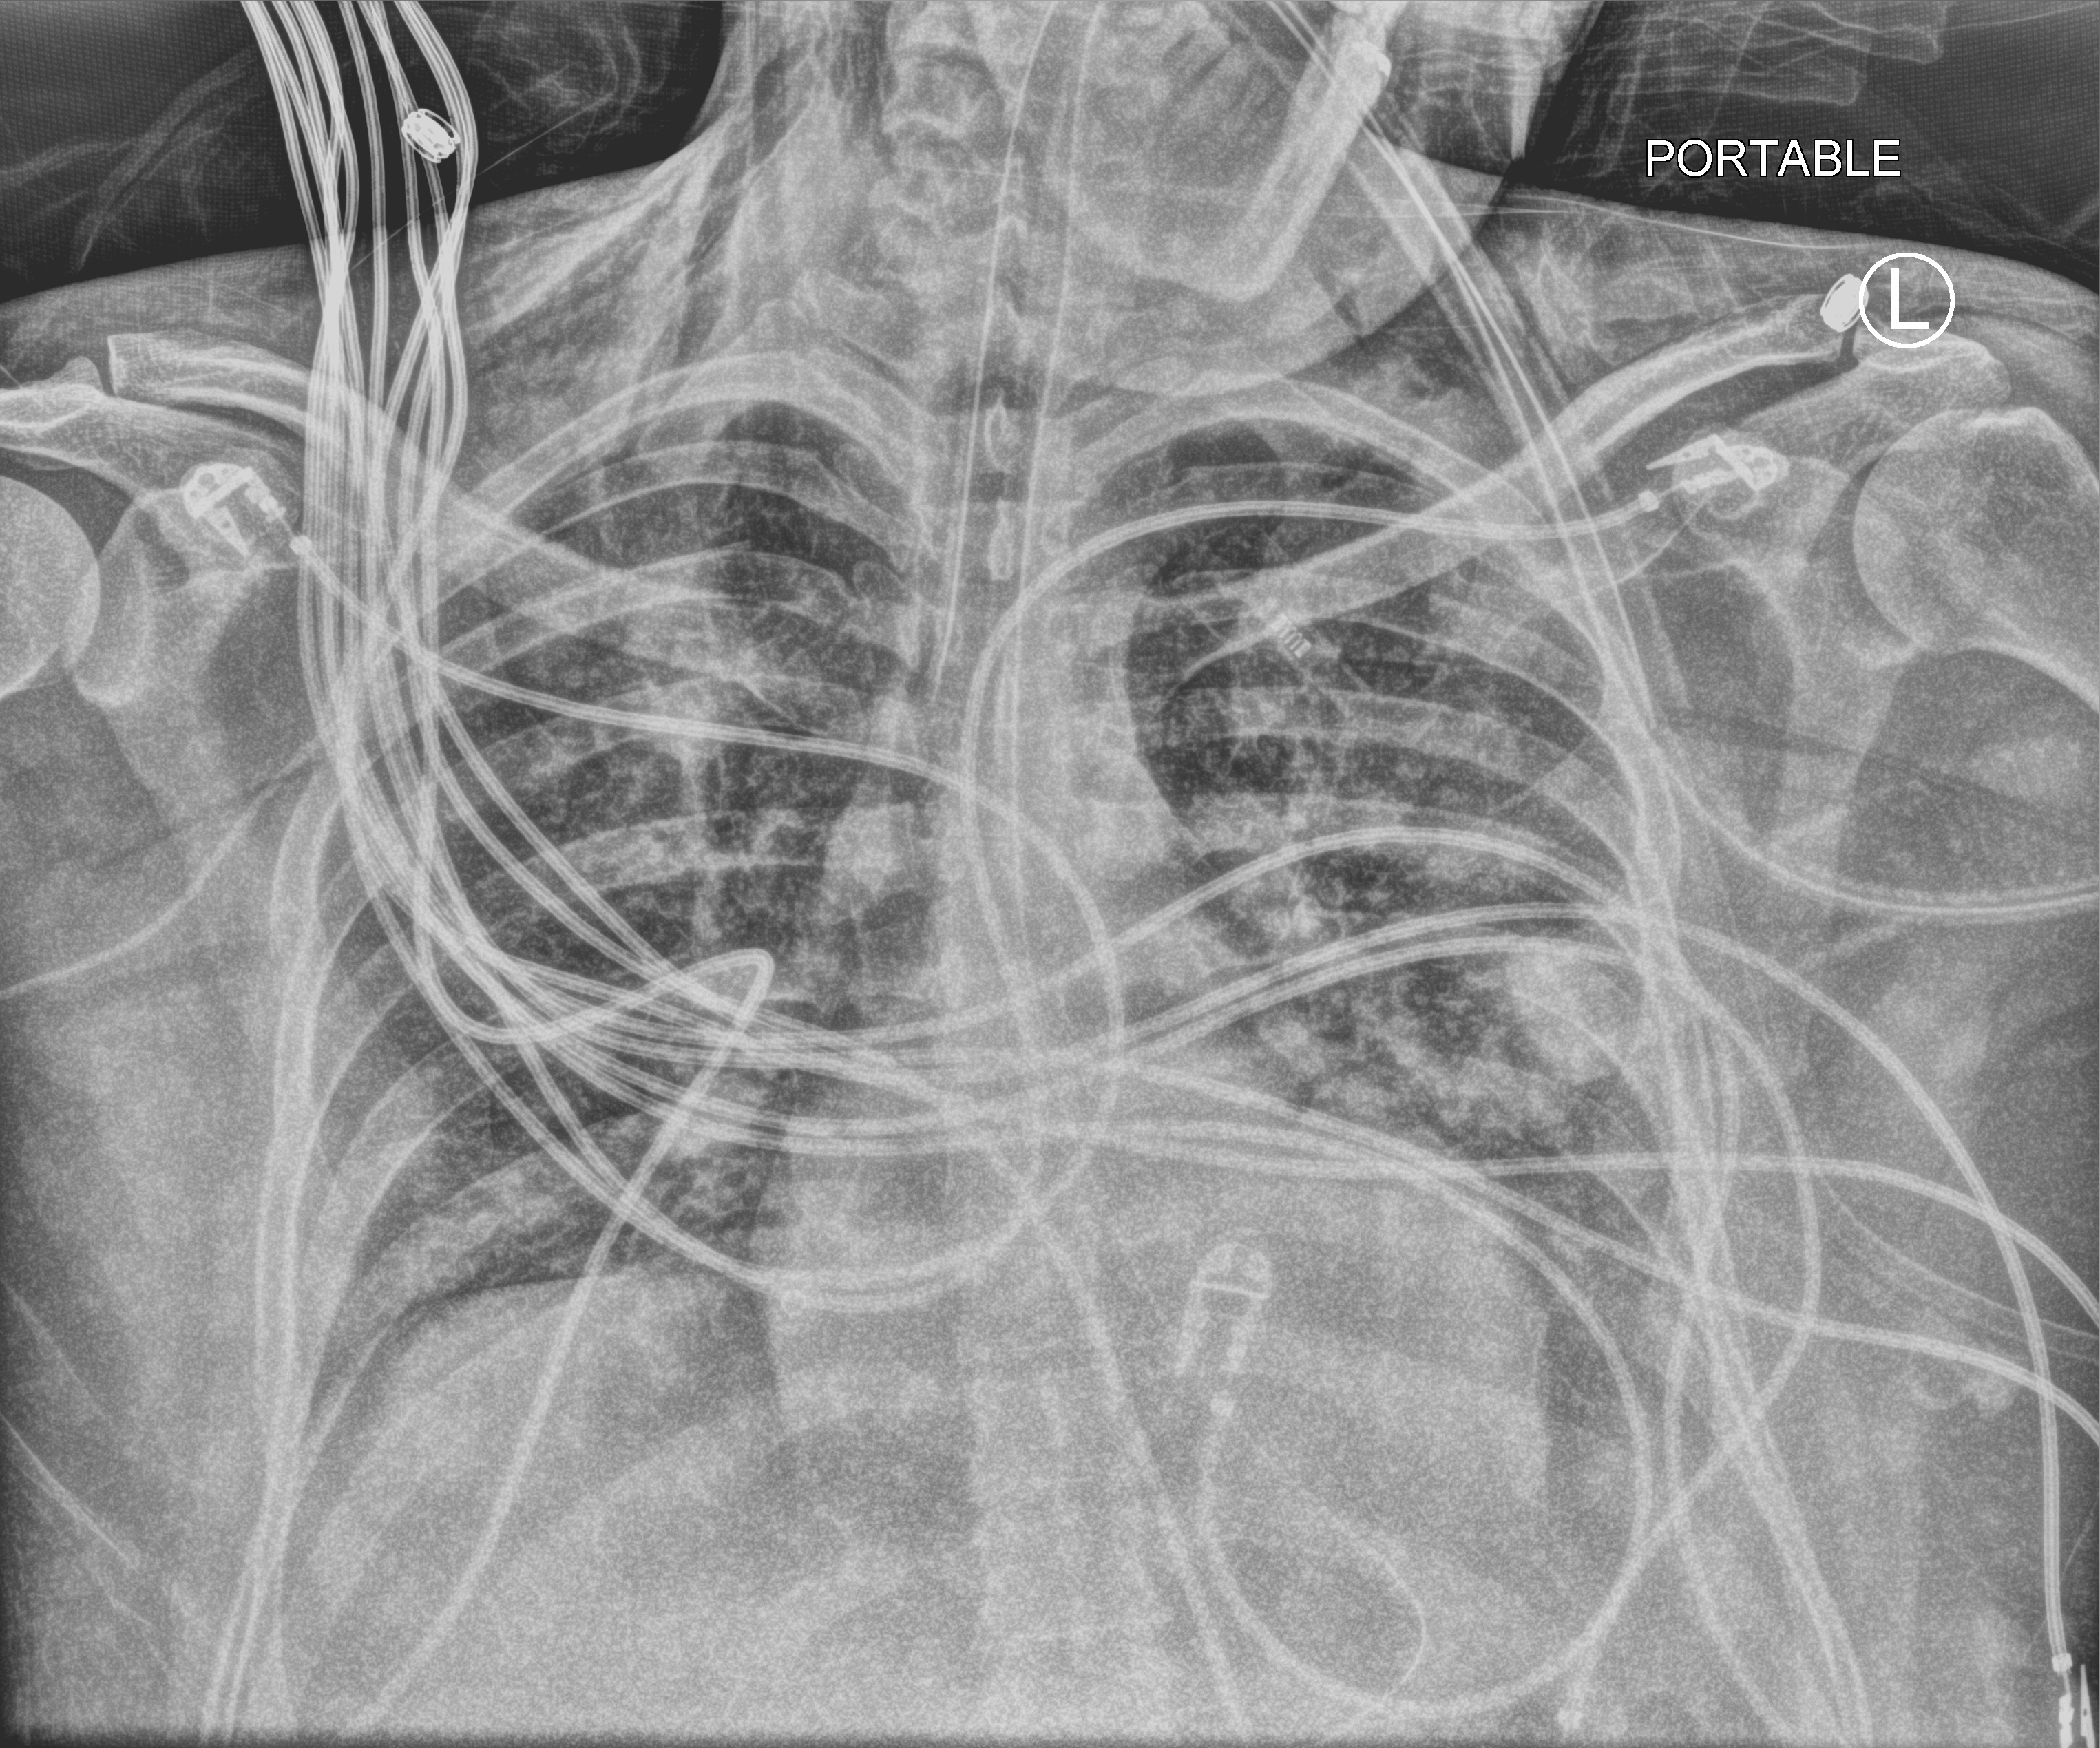
Portable chest radiograph; anteroposterior (AP) projection. Male patient hospitalised with COVID-19, age 18–59 years.
From the hospital-stay record, not from the radiograph (when in the stay this image was taken is not recorded):
- length of hospital stay: 22 days
- COPD (admission record): no